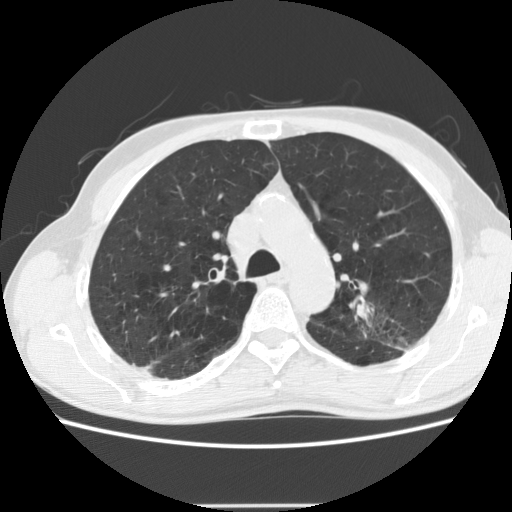
Chest CT (low-dose screening protocol), one axial image; first (baseline) screen; lung window (W 1500 / L -600 HU); slice 54 of 191 in the series. Male, age 64 years at enrolment. Current smoker at enrolment.
• Lesion marked by an expert reader, box from (x=337, y=278) to (x=444, y=361) px.
• Reader record for this screening exam (exam-level; its link to the box is not recorded): non-calcified nodule or mass ≥4 mm, left upper lobe, 27 × 19 mm, poorly defined margins, soft tissue attenuation.
• Official screen result: positive, change unspecified: nodule(s) >= 4 mm or enlarging nodule(s), mass(es), or other non-specific abnormalities suspicious for lung cancer.
• Lung cancer was diagnosed 23 days after this screen: adenocarcinoma, NOS, left upper lobe, moderately differentiated (G2), stage IA (AJCC 6th edition), 29 mm at pathology.